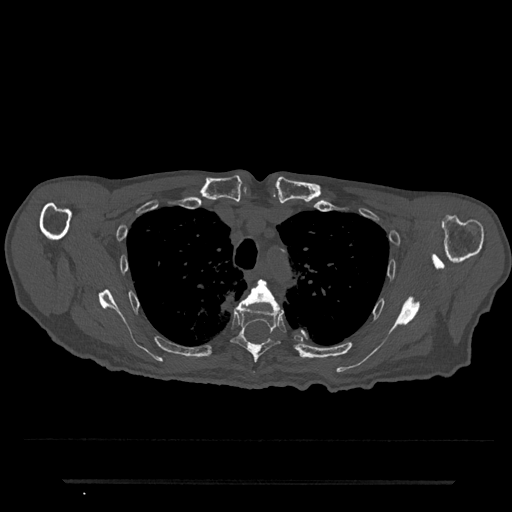
CT including the spine, one axial slice. Position 586 of 797 along the scan axis. Reconstruction kernel Br40s/3. 120 kVp. Bone window (W 1800 / L 400 HU). 512 × 512 image matrix. Male patient, age 74 years. Case-level facts recorded for this patient, not image findings: primary cancer: prostate.
Annotated regions visible in this slice (semi-automatically segmented with operator editing):
- T4 vertebra: bounding box (x1, y1, x2, y2) in pixels: (244, 280, 283, 312)
- T5 vertebra: (231, 299, 283, 363)